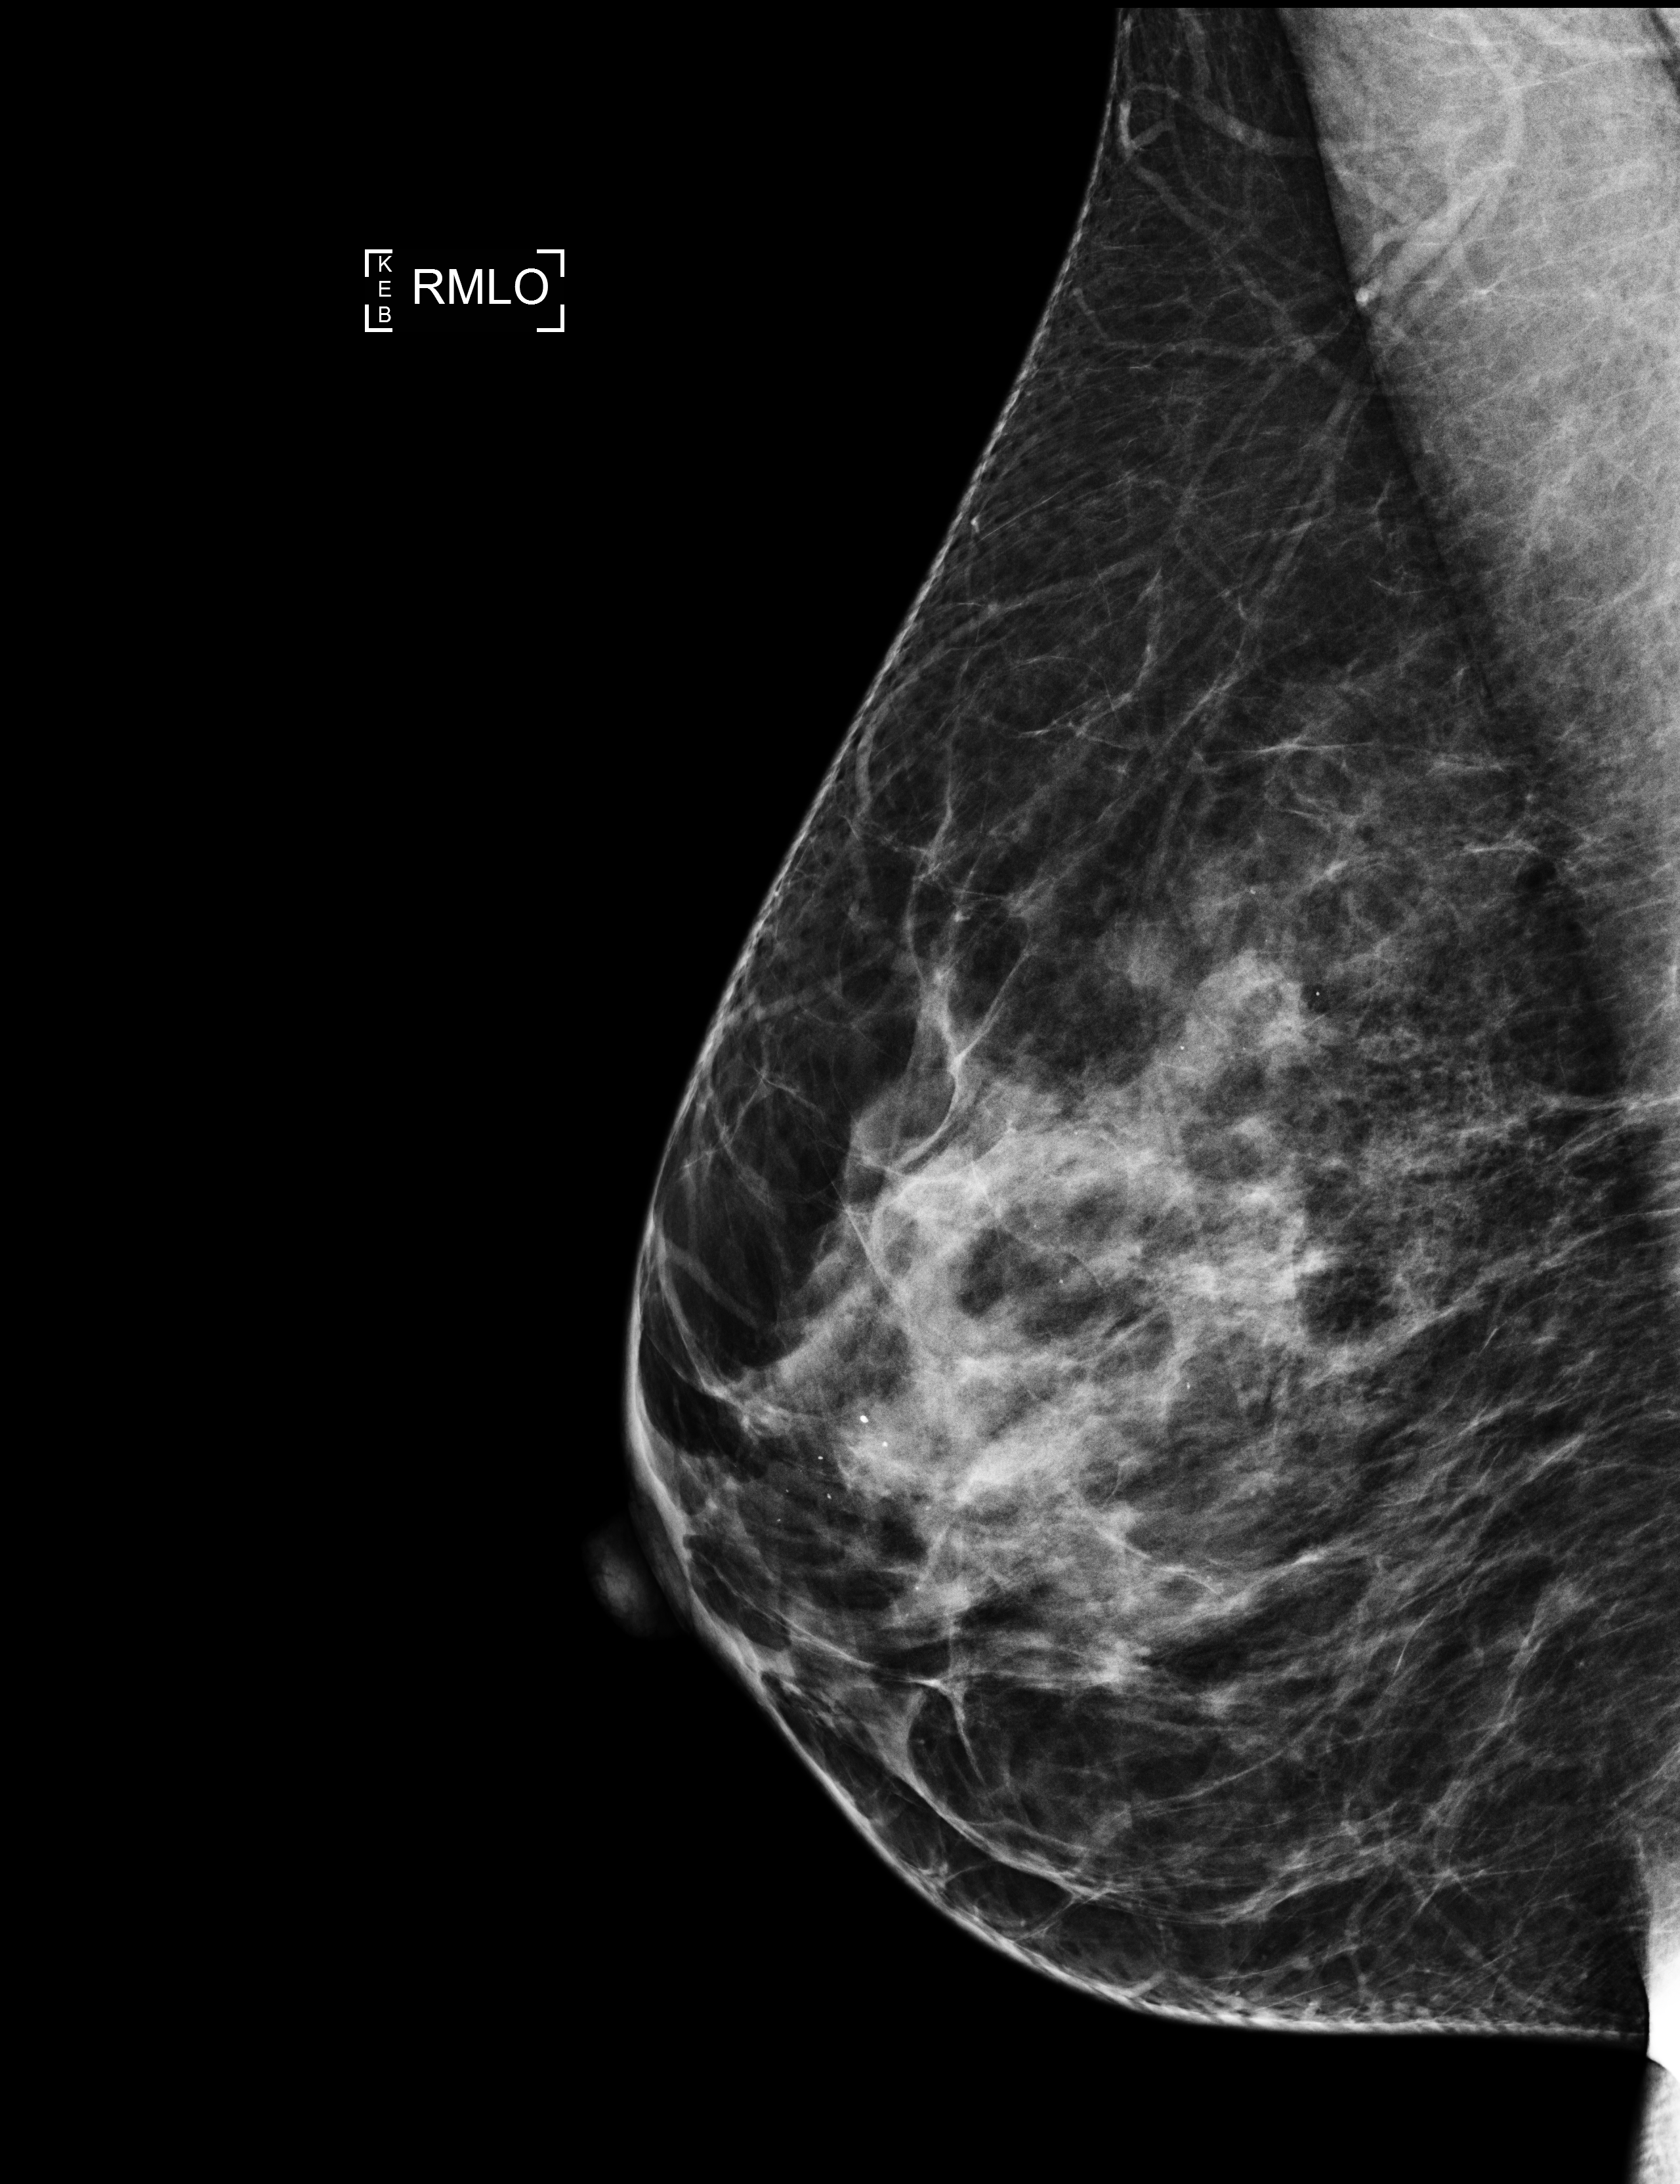
Digital mammogram (FFDM); right breast; MLO view; annual screening mammography examination; compressed breast thickness 61 mm; system: Selenia Dimensions. Patient aged 41 years (female).
- BI-RADS breast density category at the screening exam (both breasts, scale 1–4): 3
- final BI-RADS assessment for this screening round (tomosynthesis exam, both breasts): category 3
- recall: recalled for additional imaging after this screen